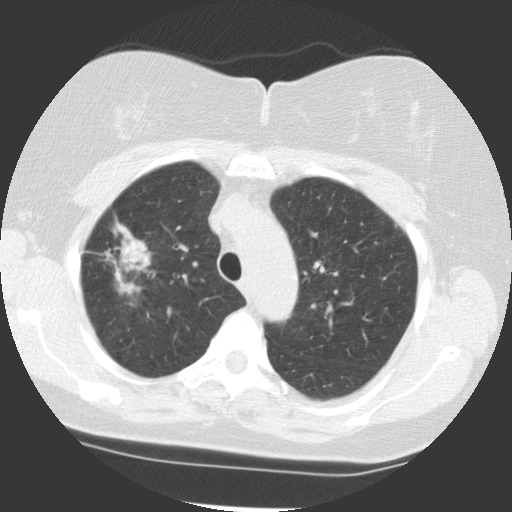
Low-dose screening chest CT, one axial slice. Slice 88 of 113 in the series (ordered by position). 140 kVp. Lung window (W 1500 / L -600 HU). 2.5 mm slice thickness. 512 × 512 image matrix, field of view 320 × 320 mm.
Structures marked on this image (manually delineated by an expert):
- lesion 1 (tumor, upper lobe of right lung): bounding box [x1, y1, x2, y2] px = [104, 219, 150, 295]